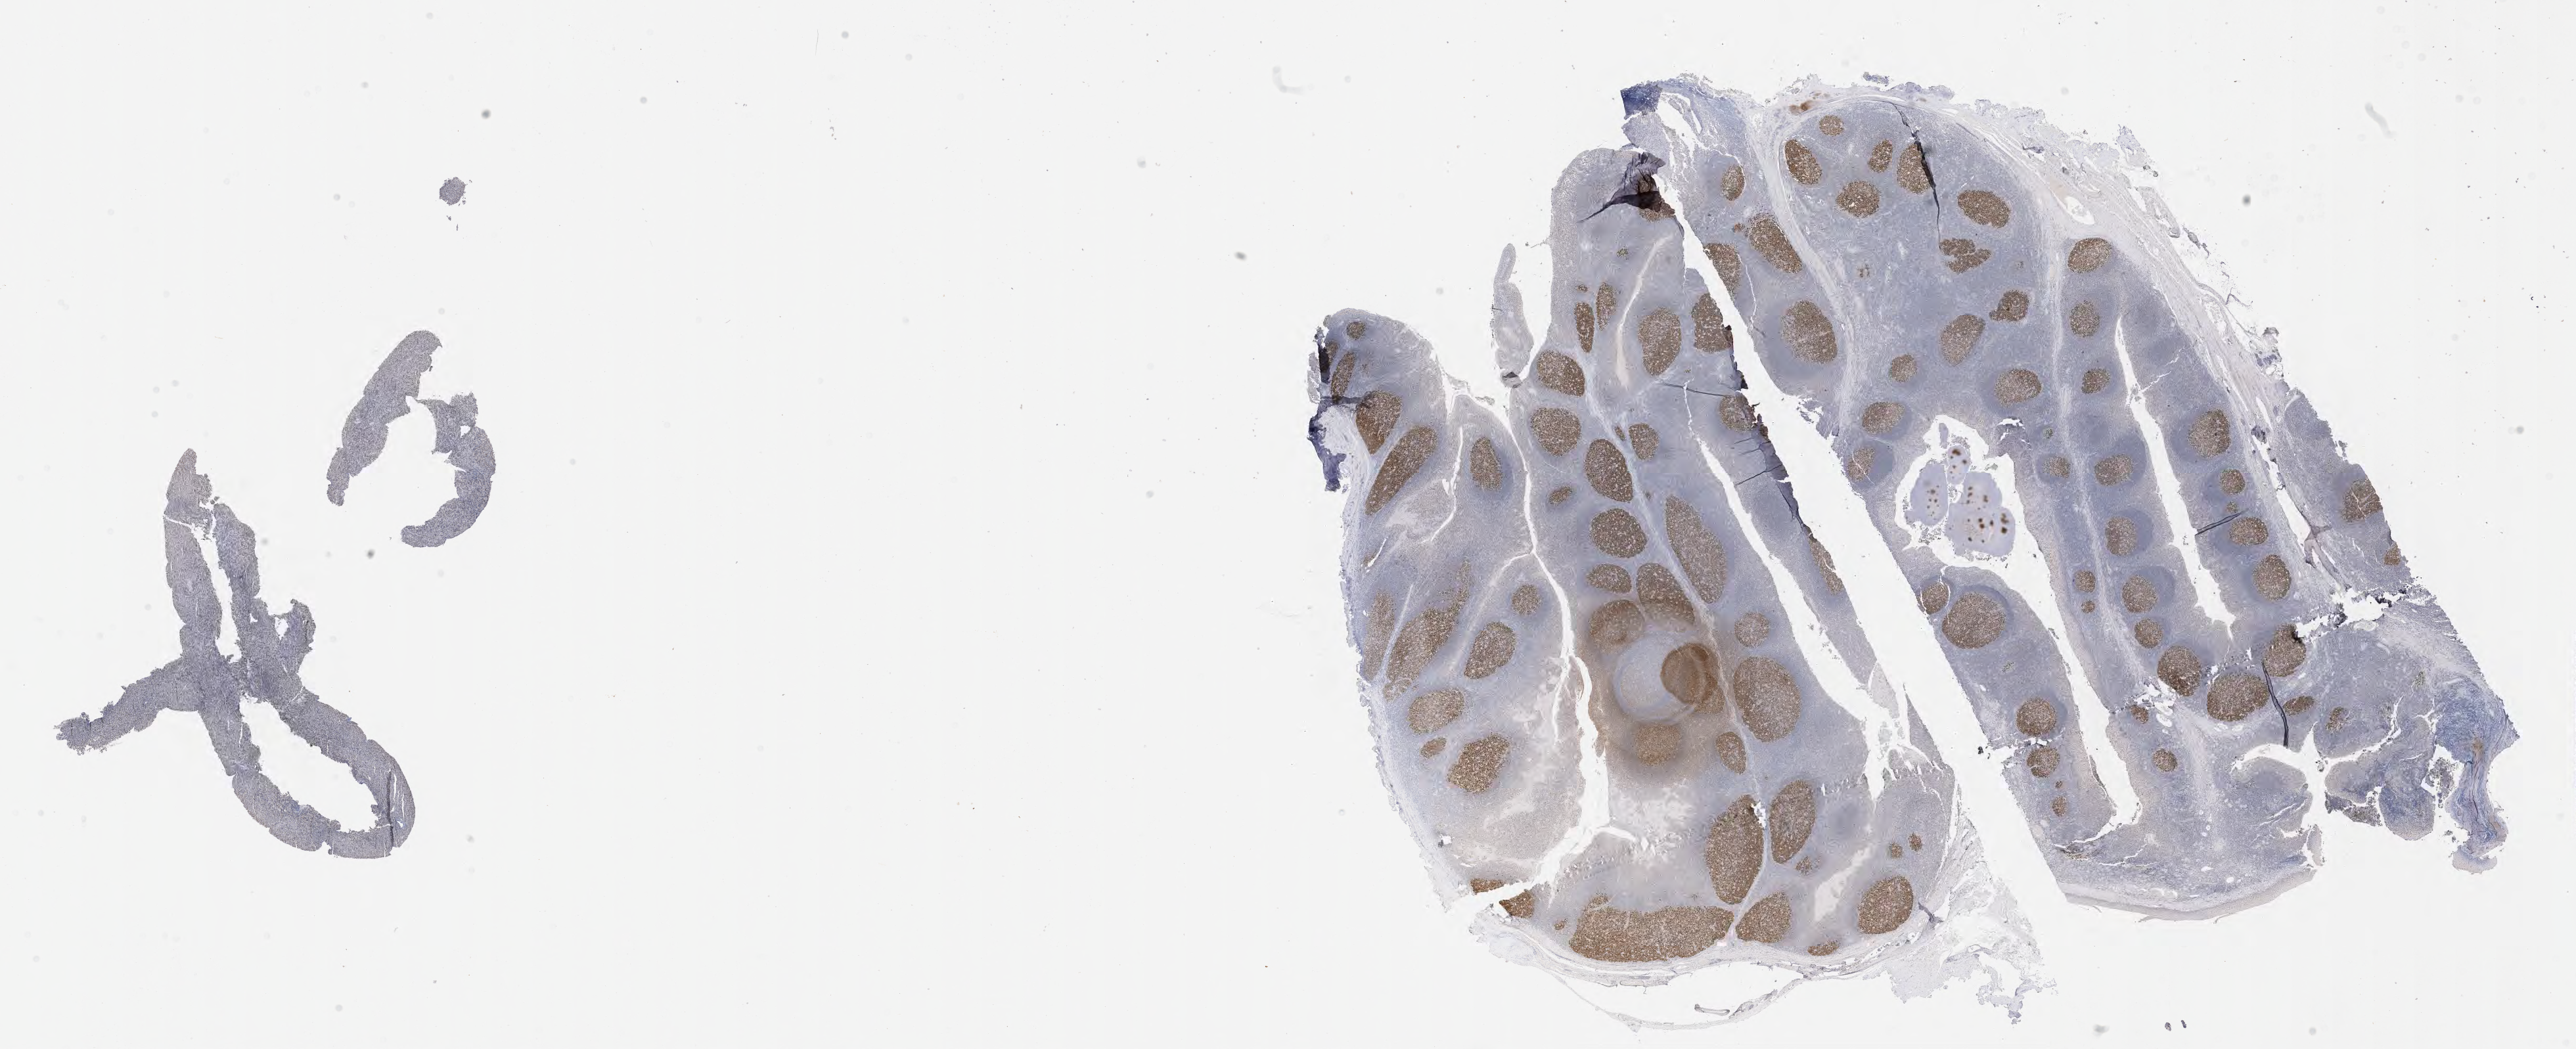
Immunohistochemistry (IHC) whole-slide image stained for BCL6 — a low-resolution overview of the entire scanned area, about 31.7 x 12.9 mm. Patient male; age 52 years.
Specimen: tumor tissue; site: liver.